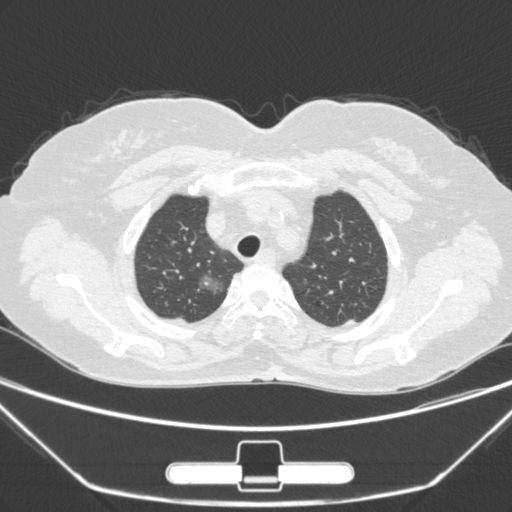
Chest CT, one axial slice; position 231 of 275 along the scan axis; lung window (W 1500 / L -600 HU); 1 mm slice thickness; 512 × 512 image matrix, field of view 356 × 356 mm. Female patient, age 63 years. Case-level facts recorded for this patient, not image findings: clinical TNM (as recorded): T1a N0 M0.
Structures marked on this image (bounding box drawn by a radiologist):
- lung tumour (recorded histology: adenocarcinoma): bounding box (x1, y1, x2, y2) in pixels: (191, 266, 232, 303)